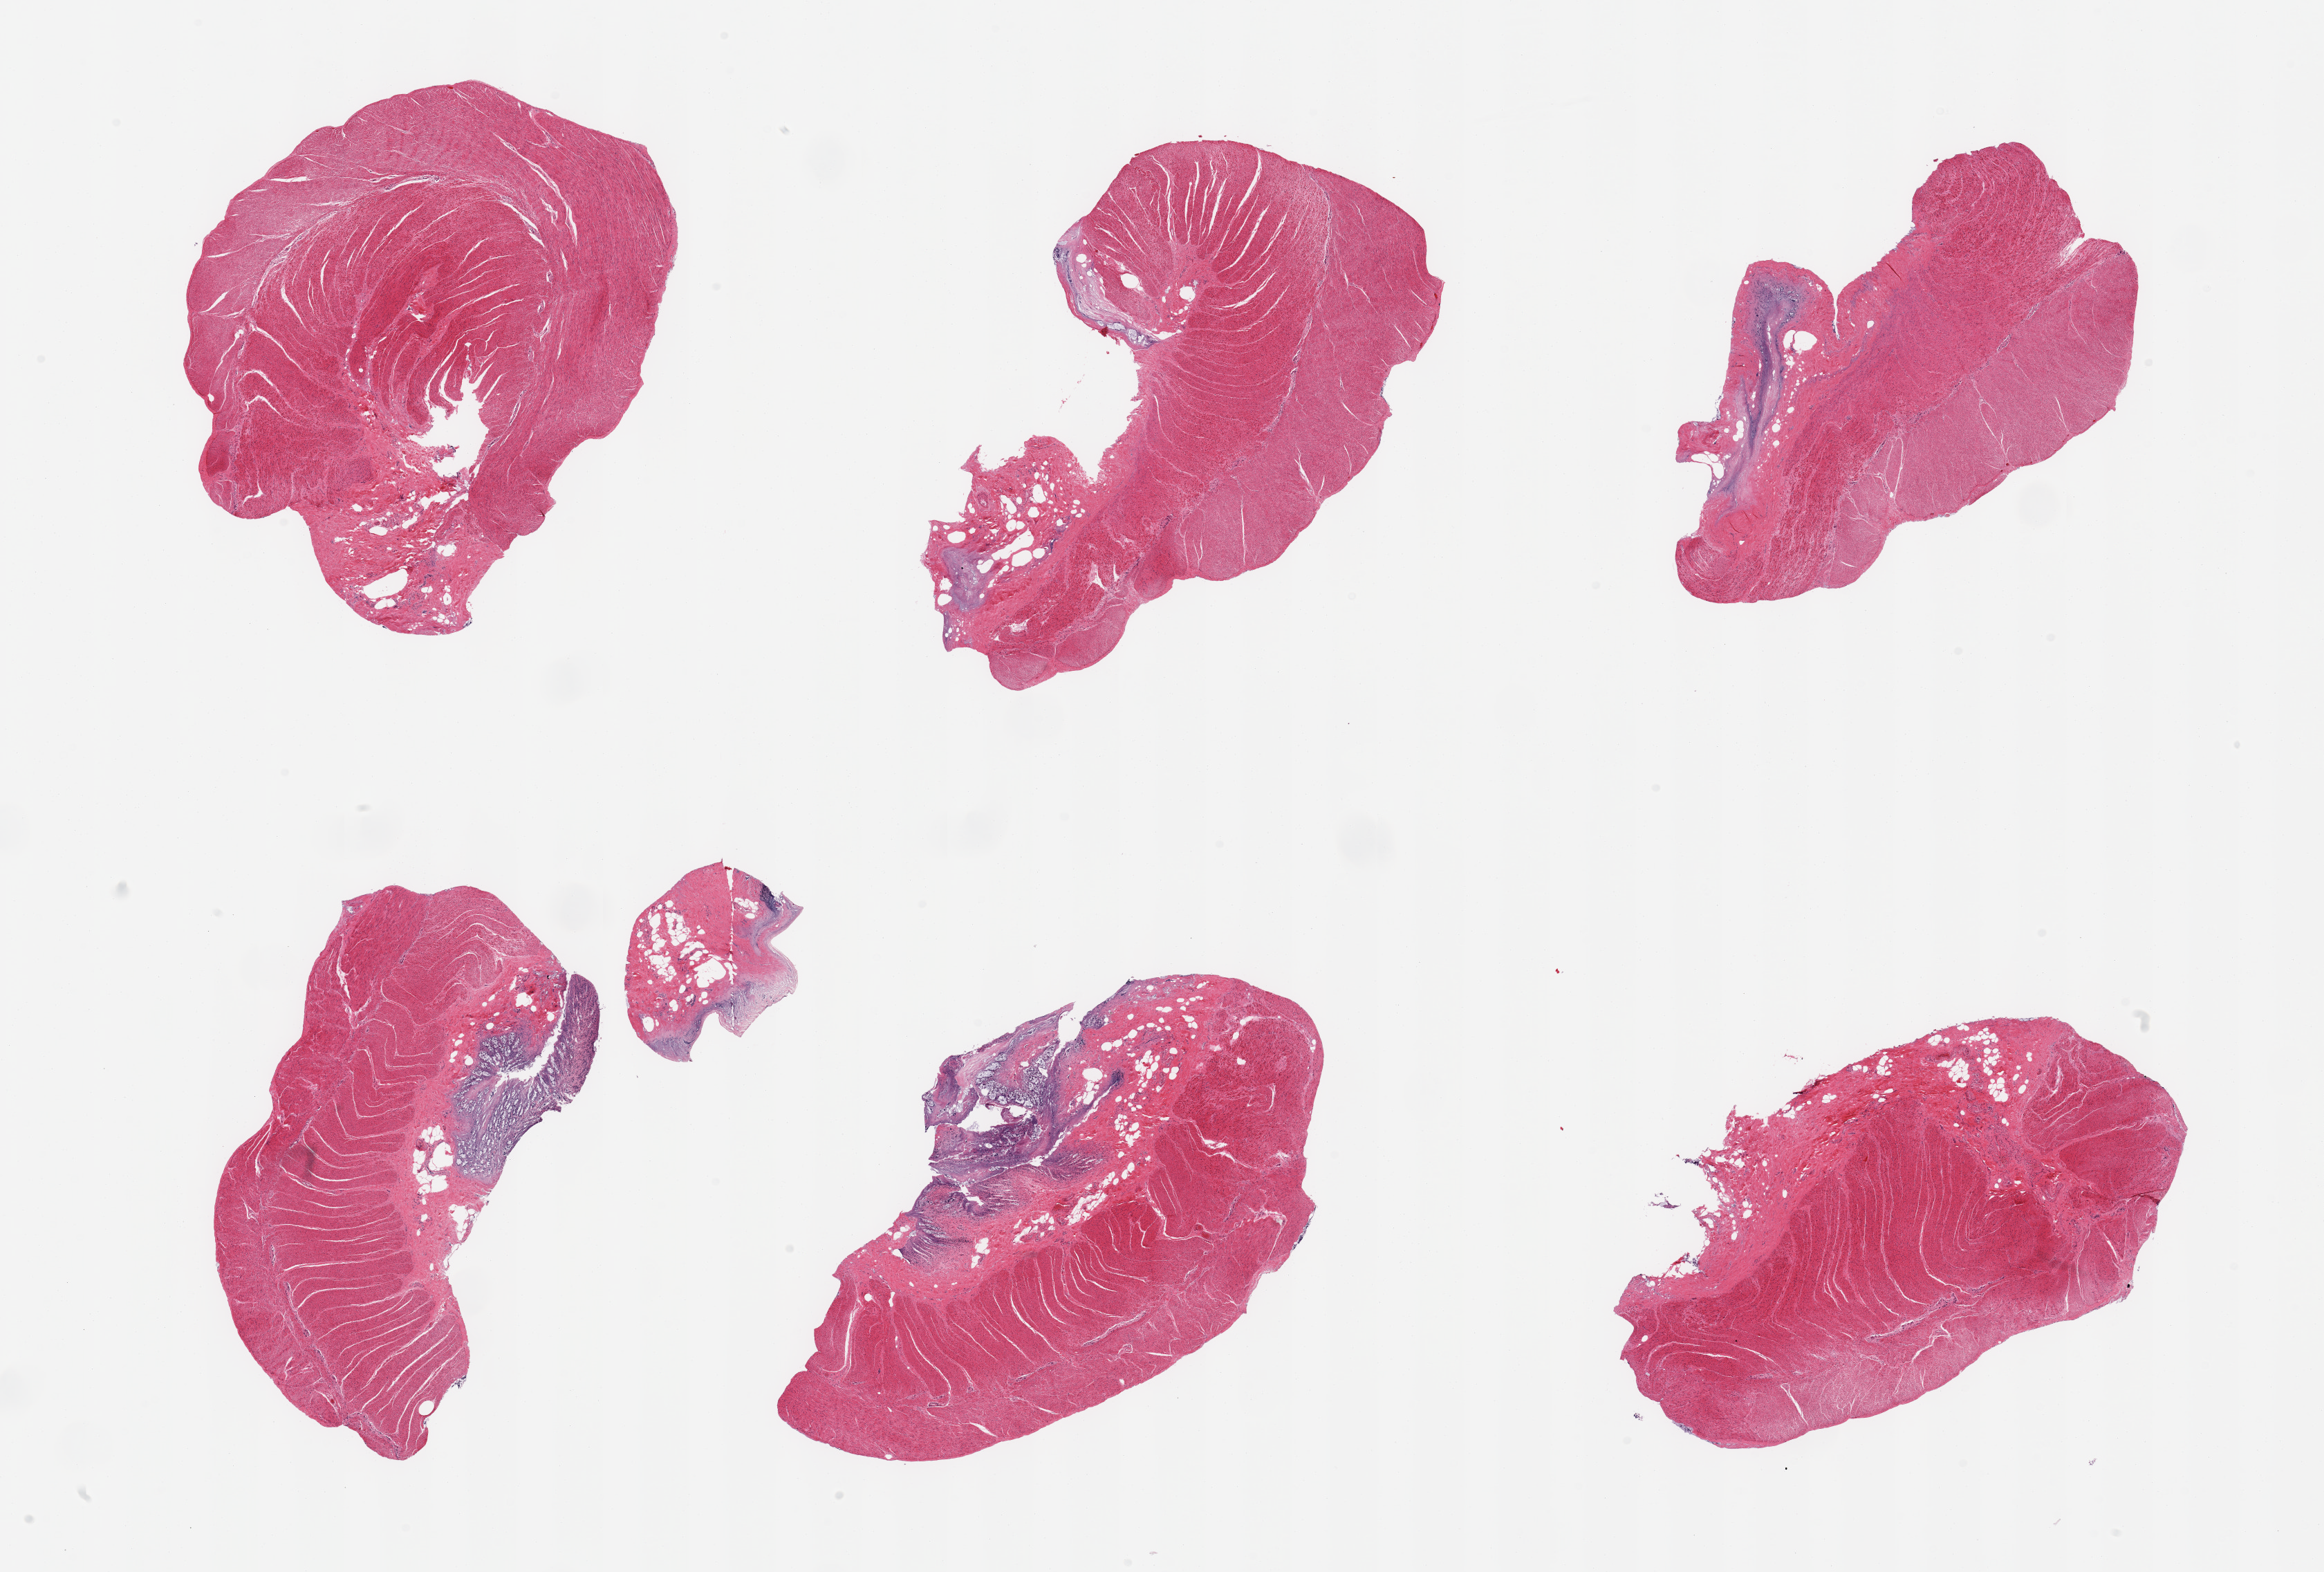
Digitized haematoxylin and eosin-stained section, brightfield, whole scanned area (about 26.6 x 18.0 mm, acquisition: 20x scan) shown as a low-resolution overview; PAXgene-fixed, paraffin-embedded tissue; target tissue: sigmoid colon; tissue donor sample. Donor sex: male.
Pathologist's review note for this sample: 6 pieces, confirmed target muscularis, trace autolyzed 'contaminant' mucosa present.